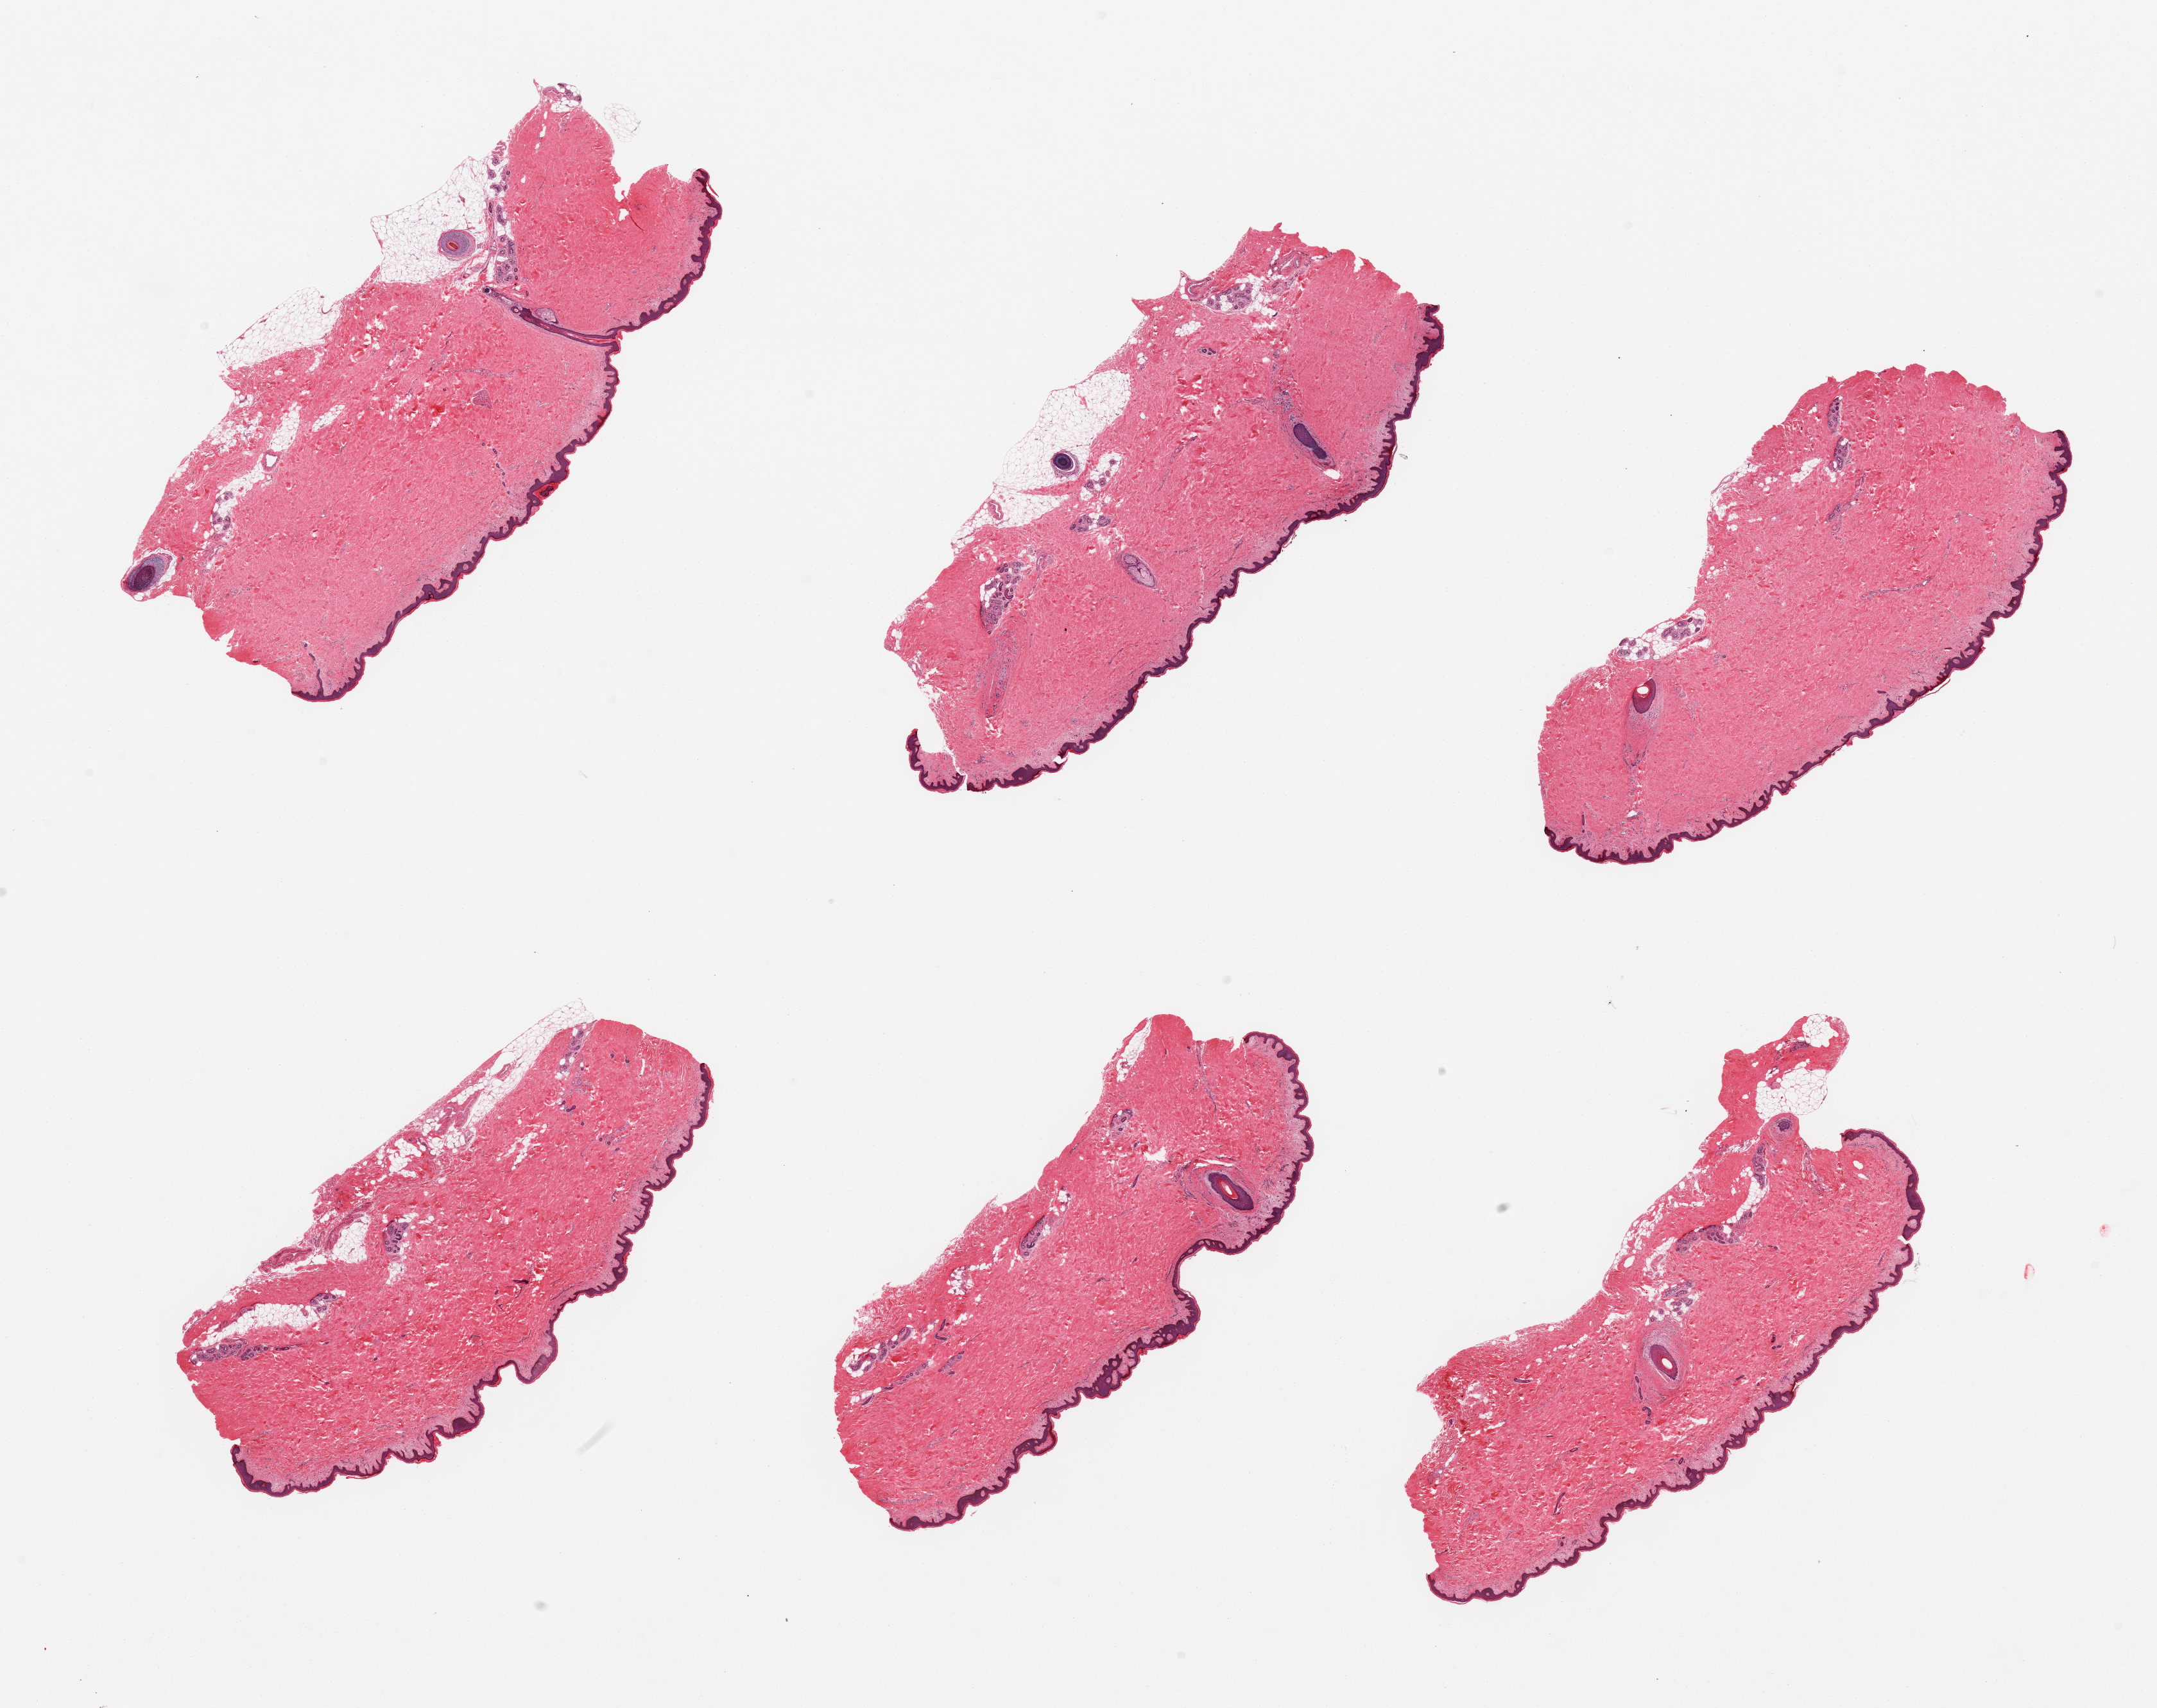
Digitized hematoxylin and eosin (H&E)-stained section — a low-resolution overview of the entire scanned area, about 26.6 x 21.0 mm; PAXgene-fixed, paraffin-embedded tissue; target tissue: skin of suprapubic region; tissue donor sample. Donor sex: male.
• pathologist's review note for this sample: 6 pieces, predominantly well trimmed, 3 include 5-10% fat